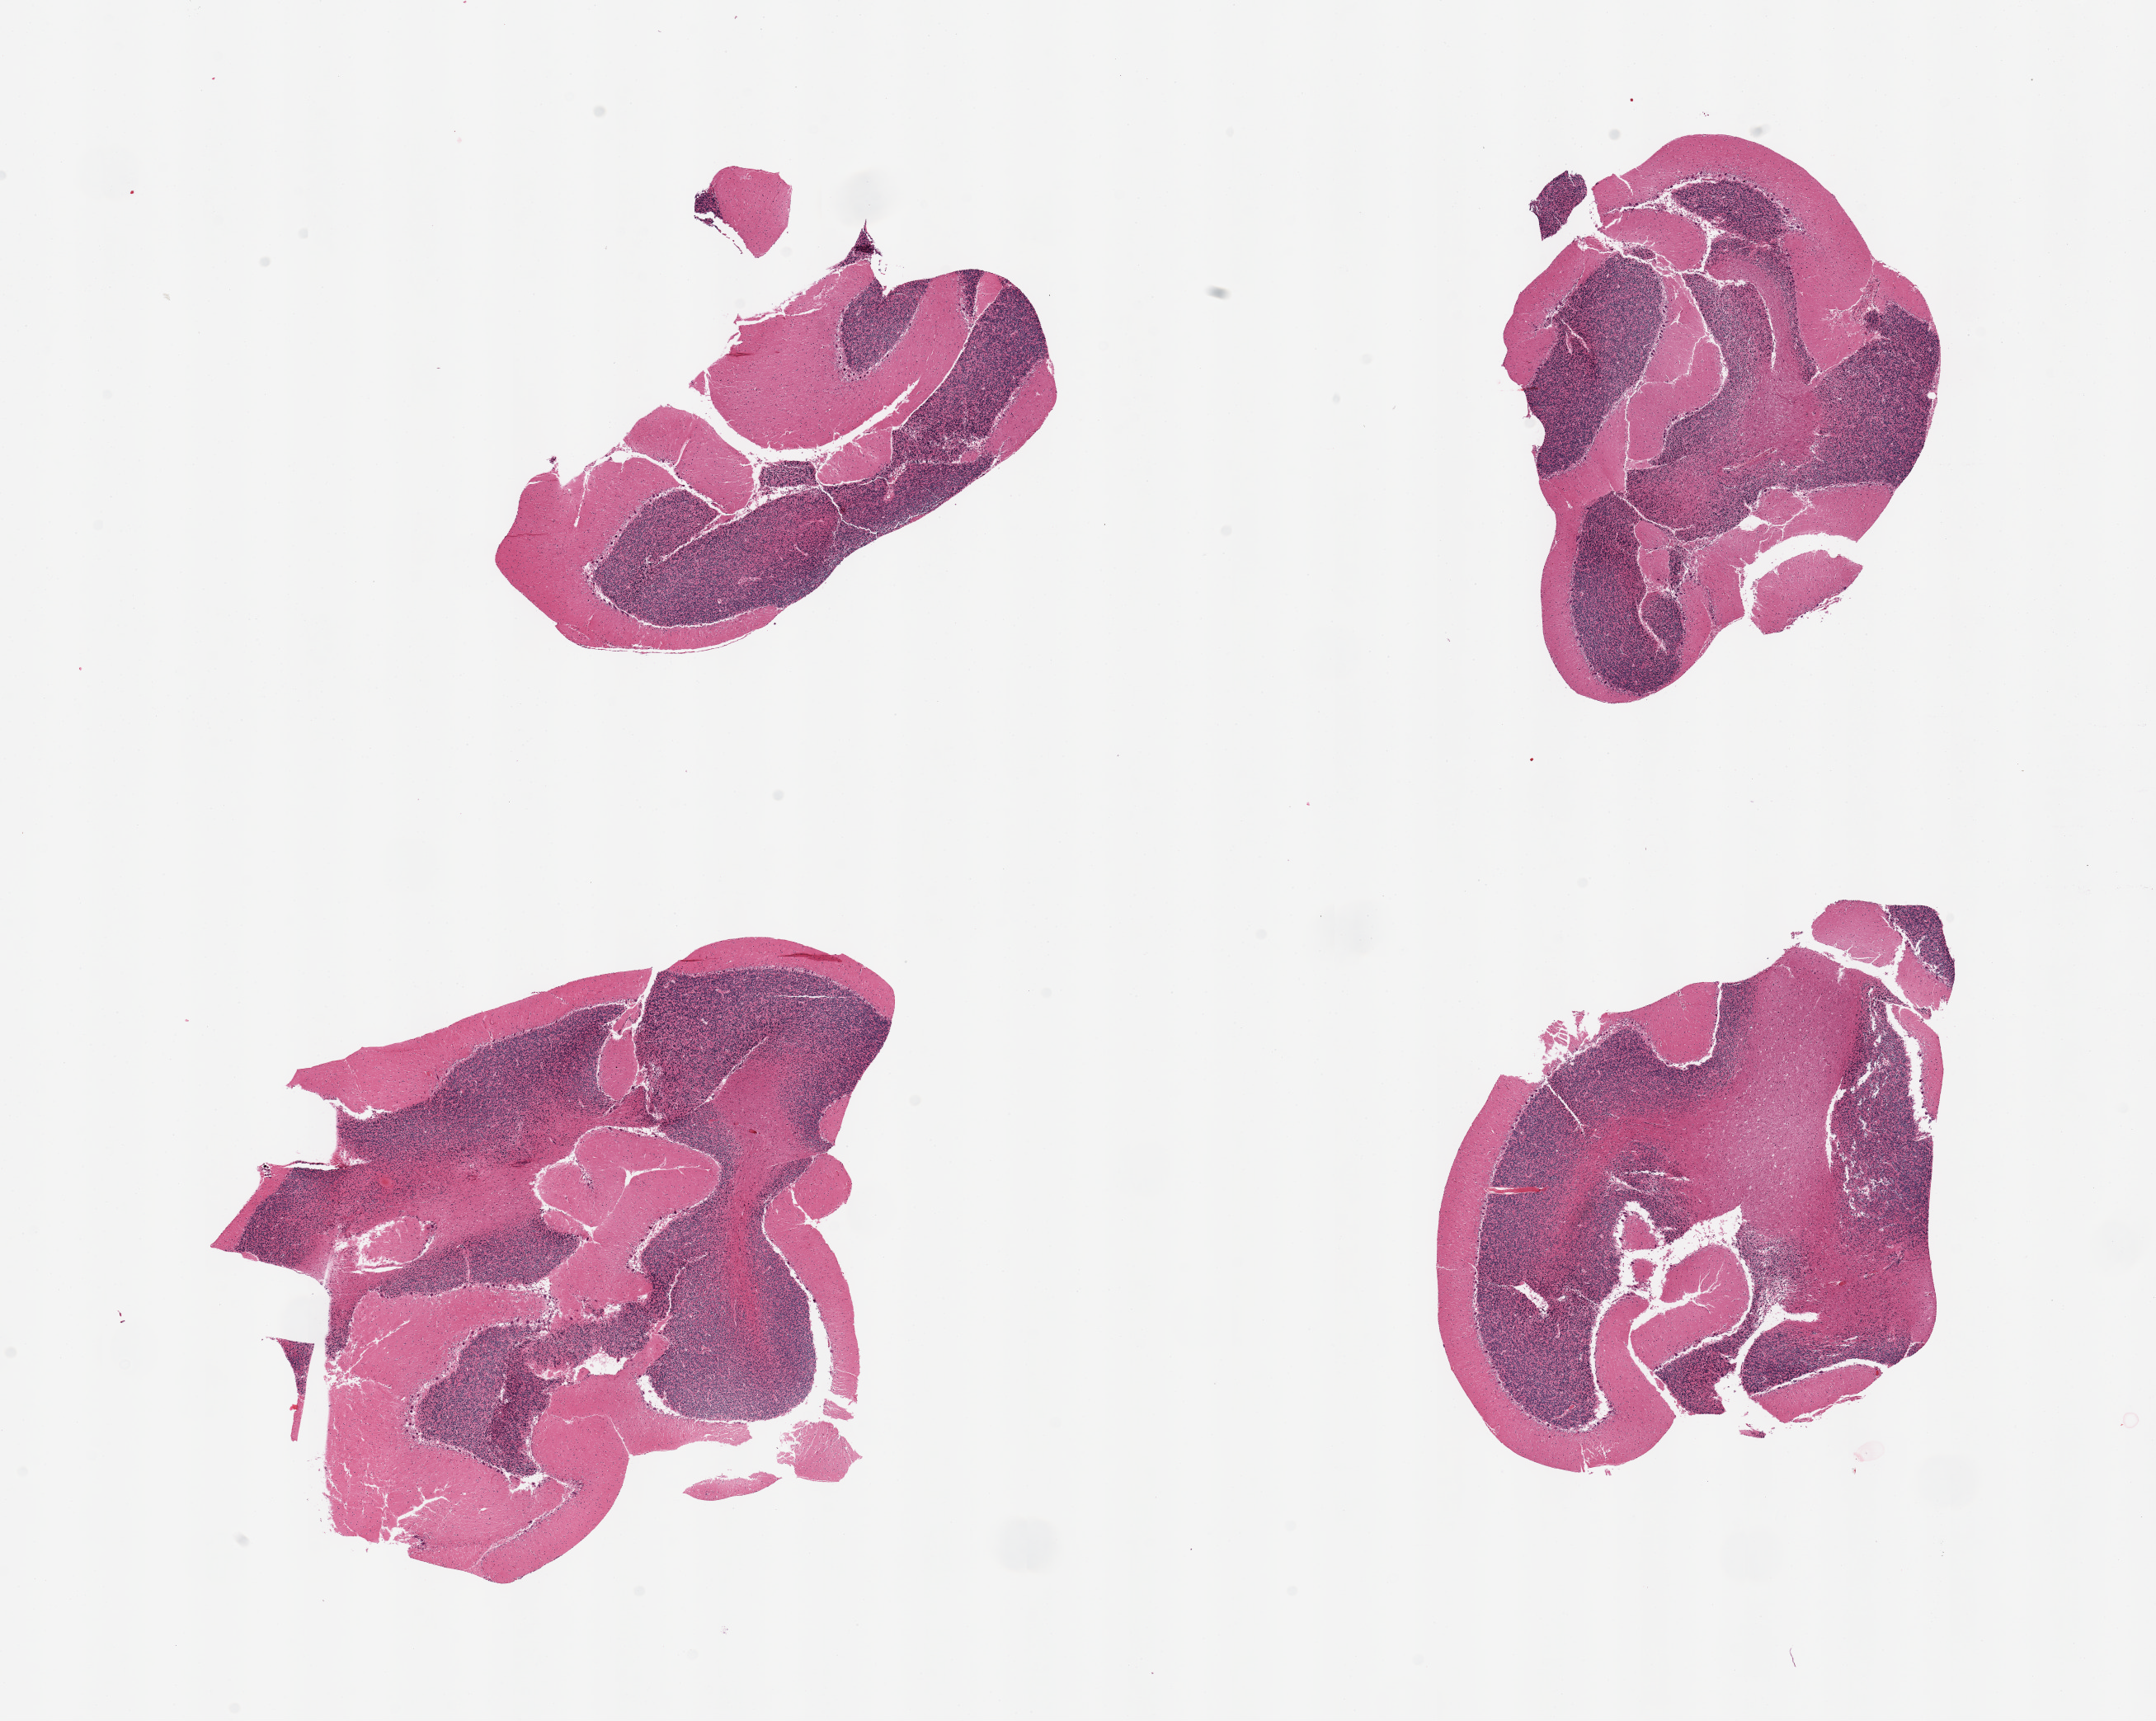
Whole-slide image, haematoxylin and eosin stain — shown as a low-resolution overview of the whole scanned area (about 20.7 x 16.5 mm), PAXgene-fixed paraffin-embedded (PFPE) section, sampled site (target tissue): cerebellum, donor tissue sample. Donor: male.
Pathologist's review note for this sample: 4 pieces.